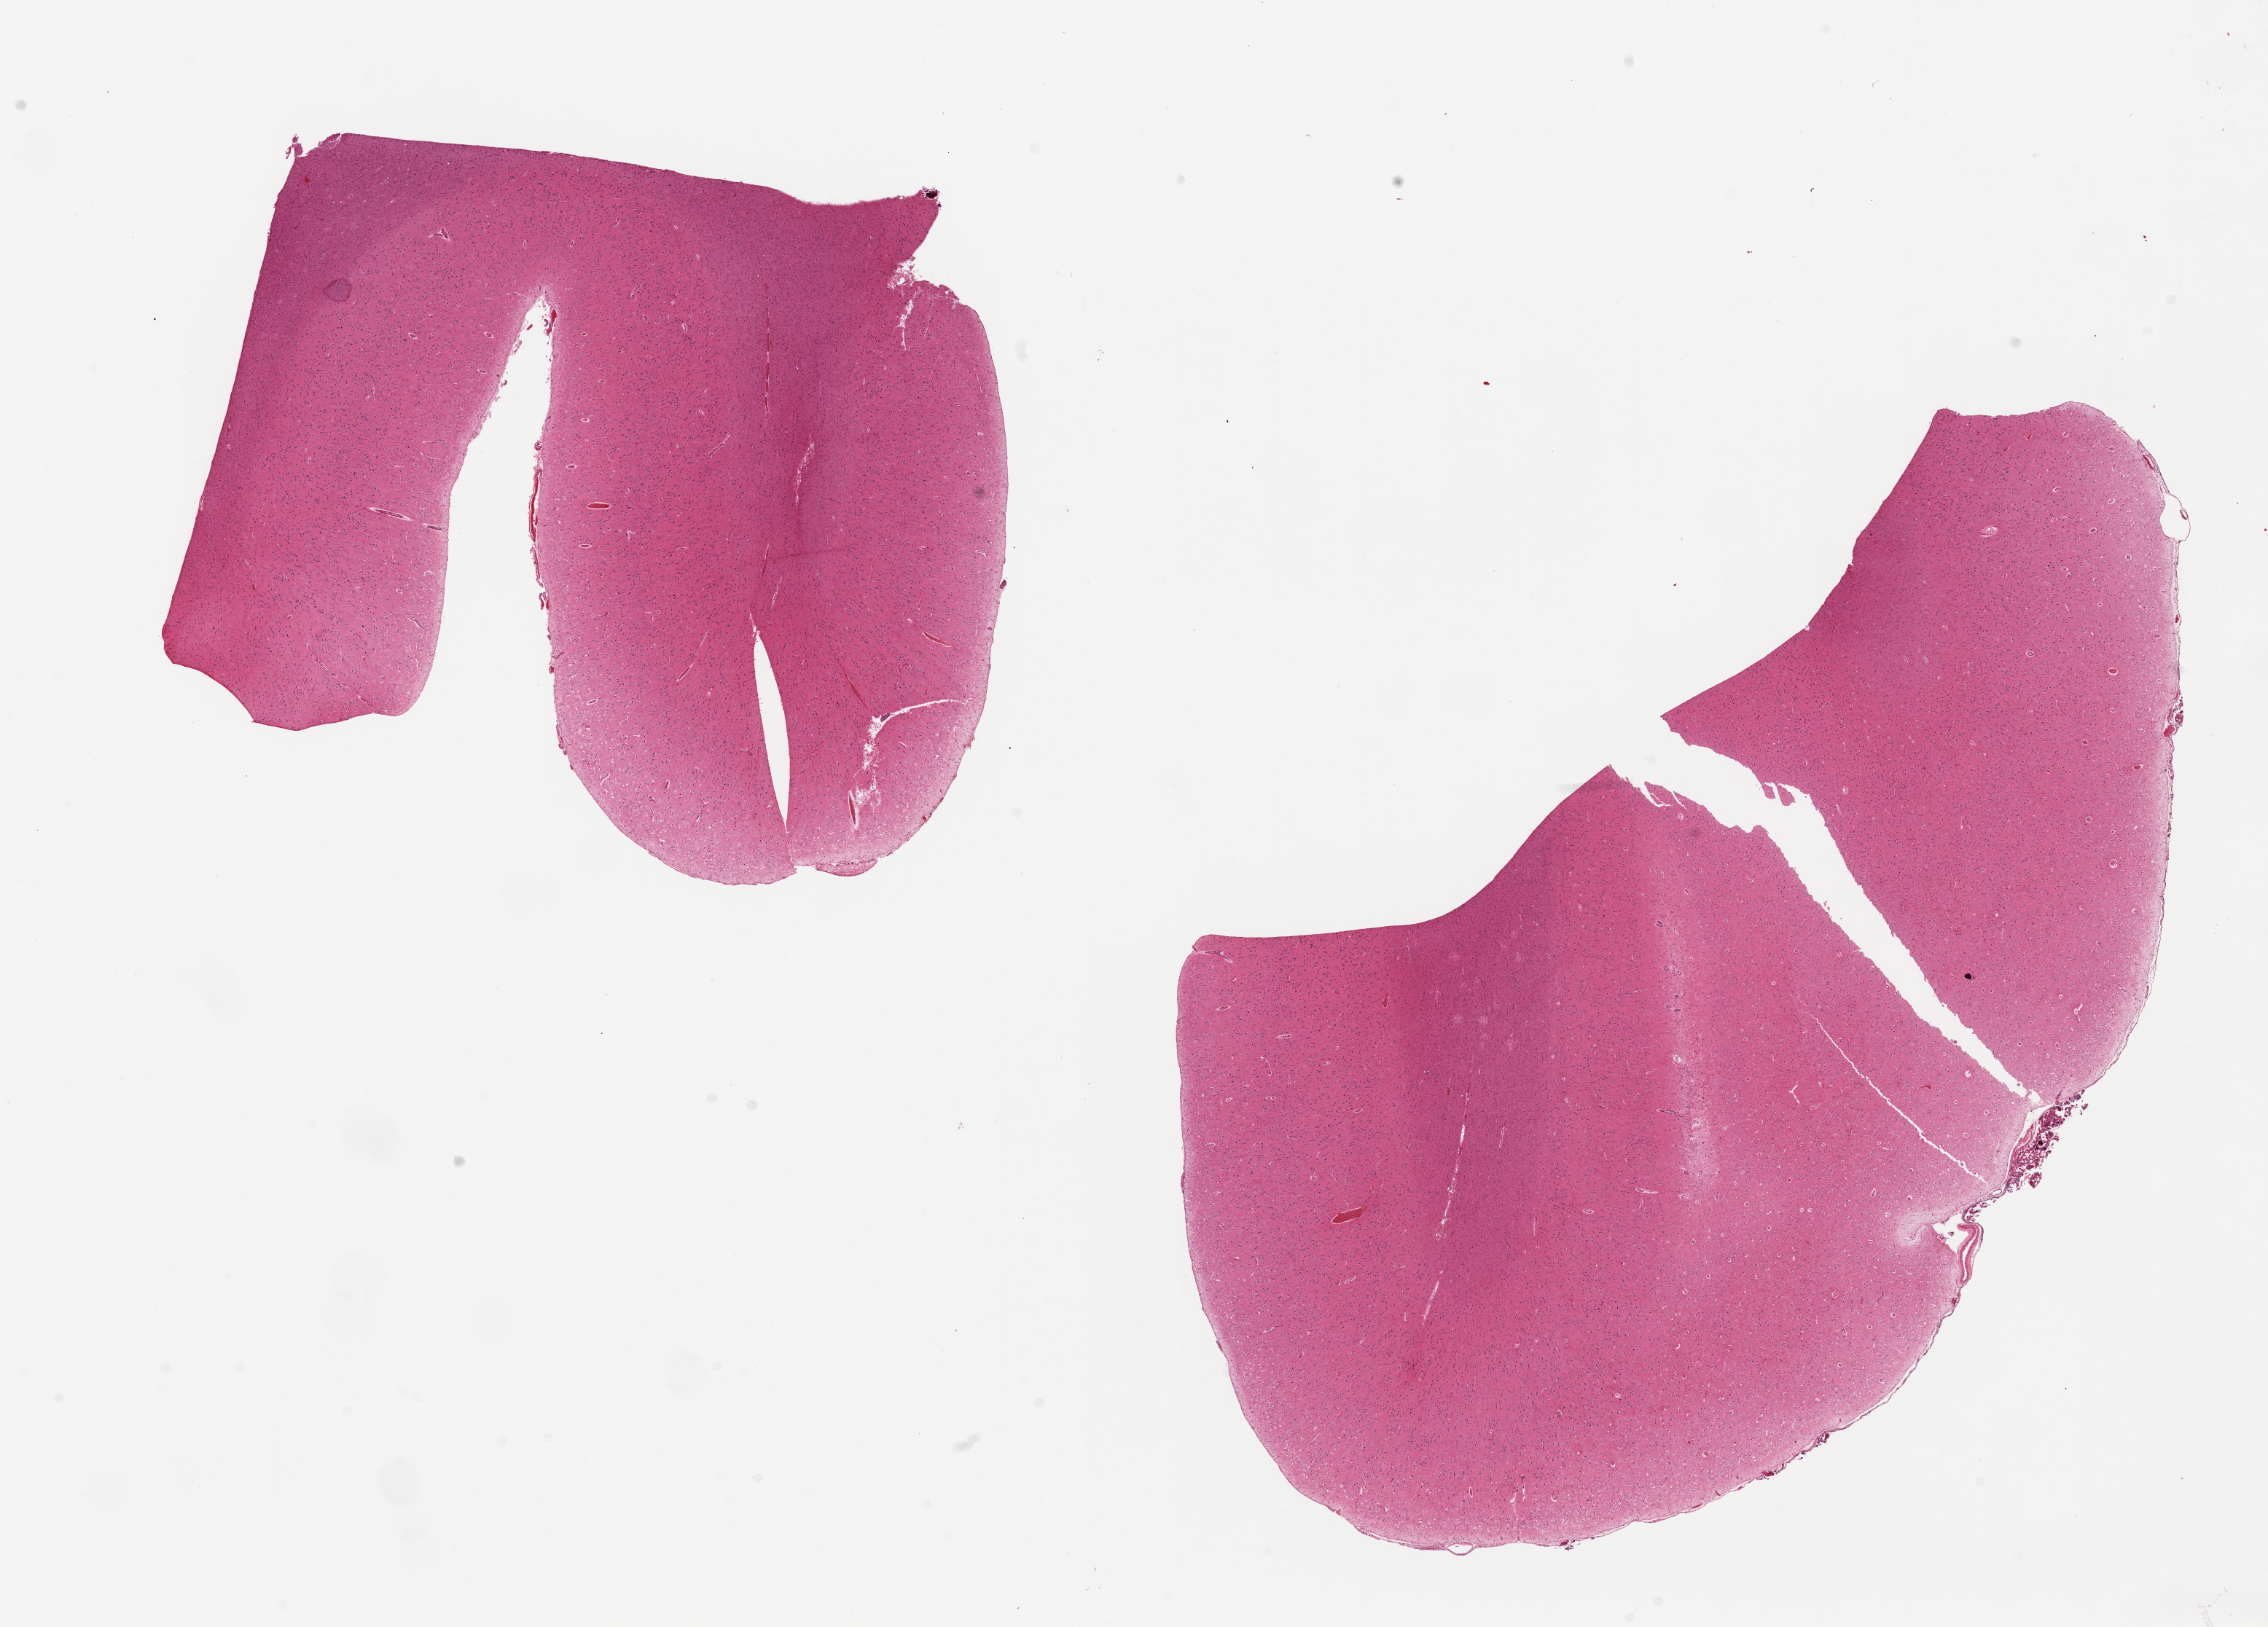
Digitized H&E-stained section — low-resolution overview of the scanned area, about 24.6 x 17.7 mm. PAXgene-fixed paraffin-embedded (PFPE) section. Section of cerebral cortex (target tissue). Tissue donor sample. Donor sex: male.
- reviewer comment on this tissue sample: 2 pieces, no abnormalities